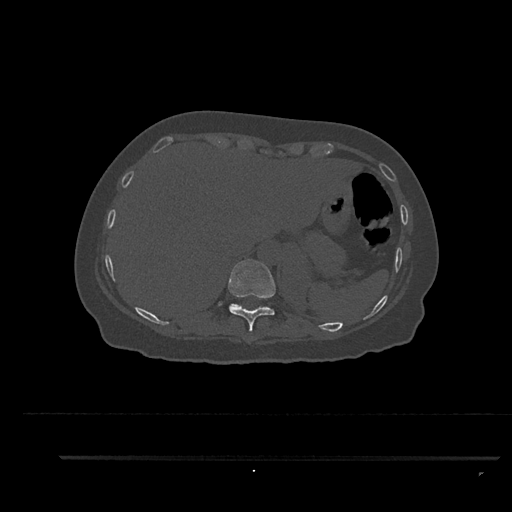
CT including the spine, one axial slice; slice 356 of 797 in the series (ordered by position); 120 kVp; bone window (W 1800 / L 400 HU); 0.5 mm slice thickness; 512 × 512 image matrix. Patient: female, 44 years. Case-level facts recorded for this patient, not image findings: primary cancer: renal.
Structures marked on this image (semi-automatically segmented with operator editing):
- T10 vertebra: bounding box <228,259,276,333> (left, top, right, bottom; pixels)
- T11 vertebra: <231,304,238,305>